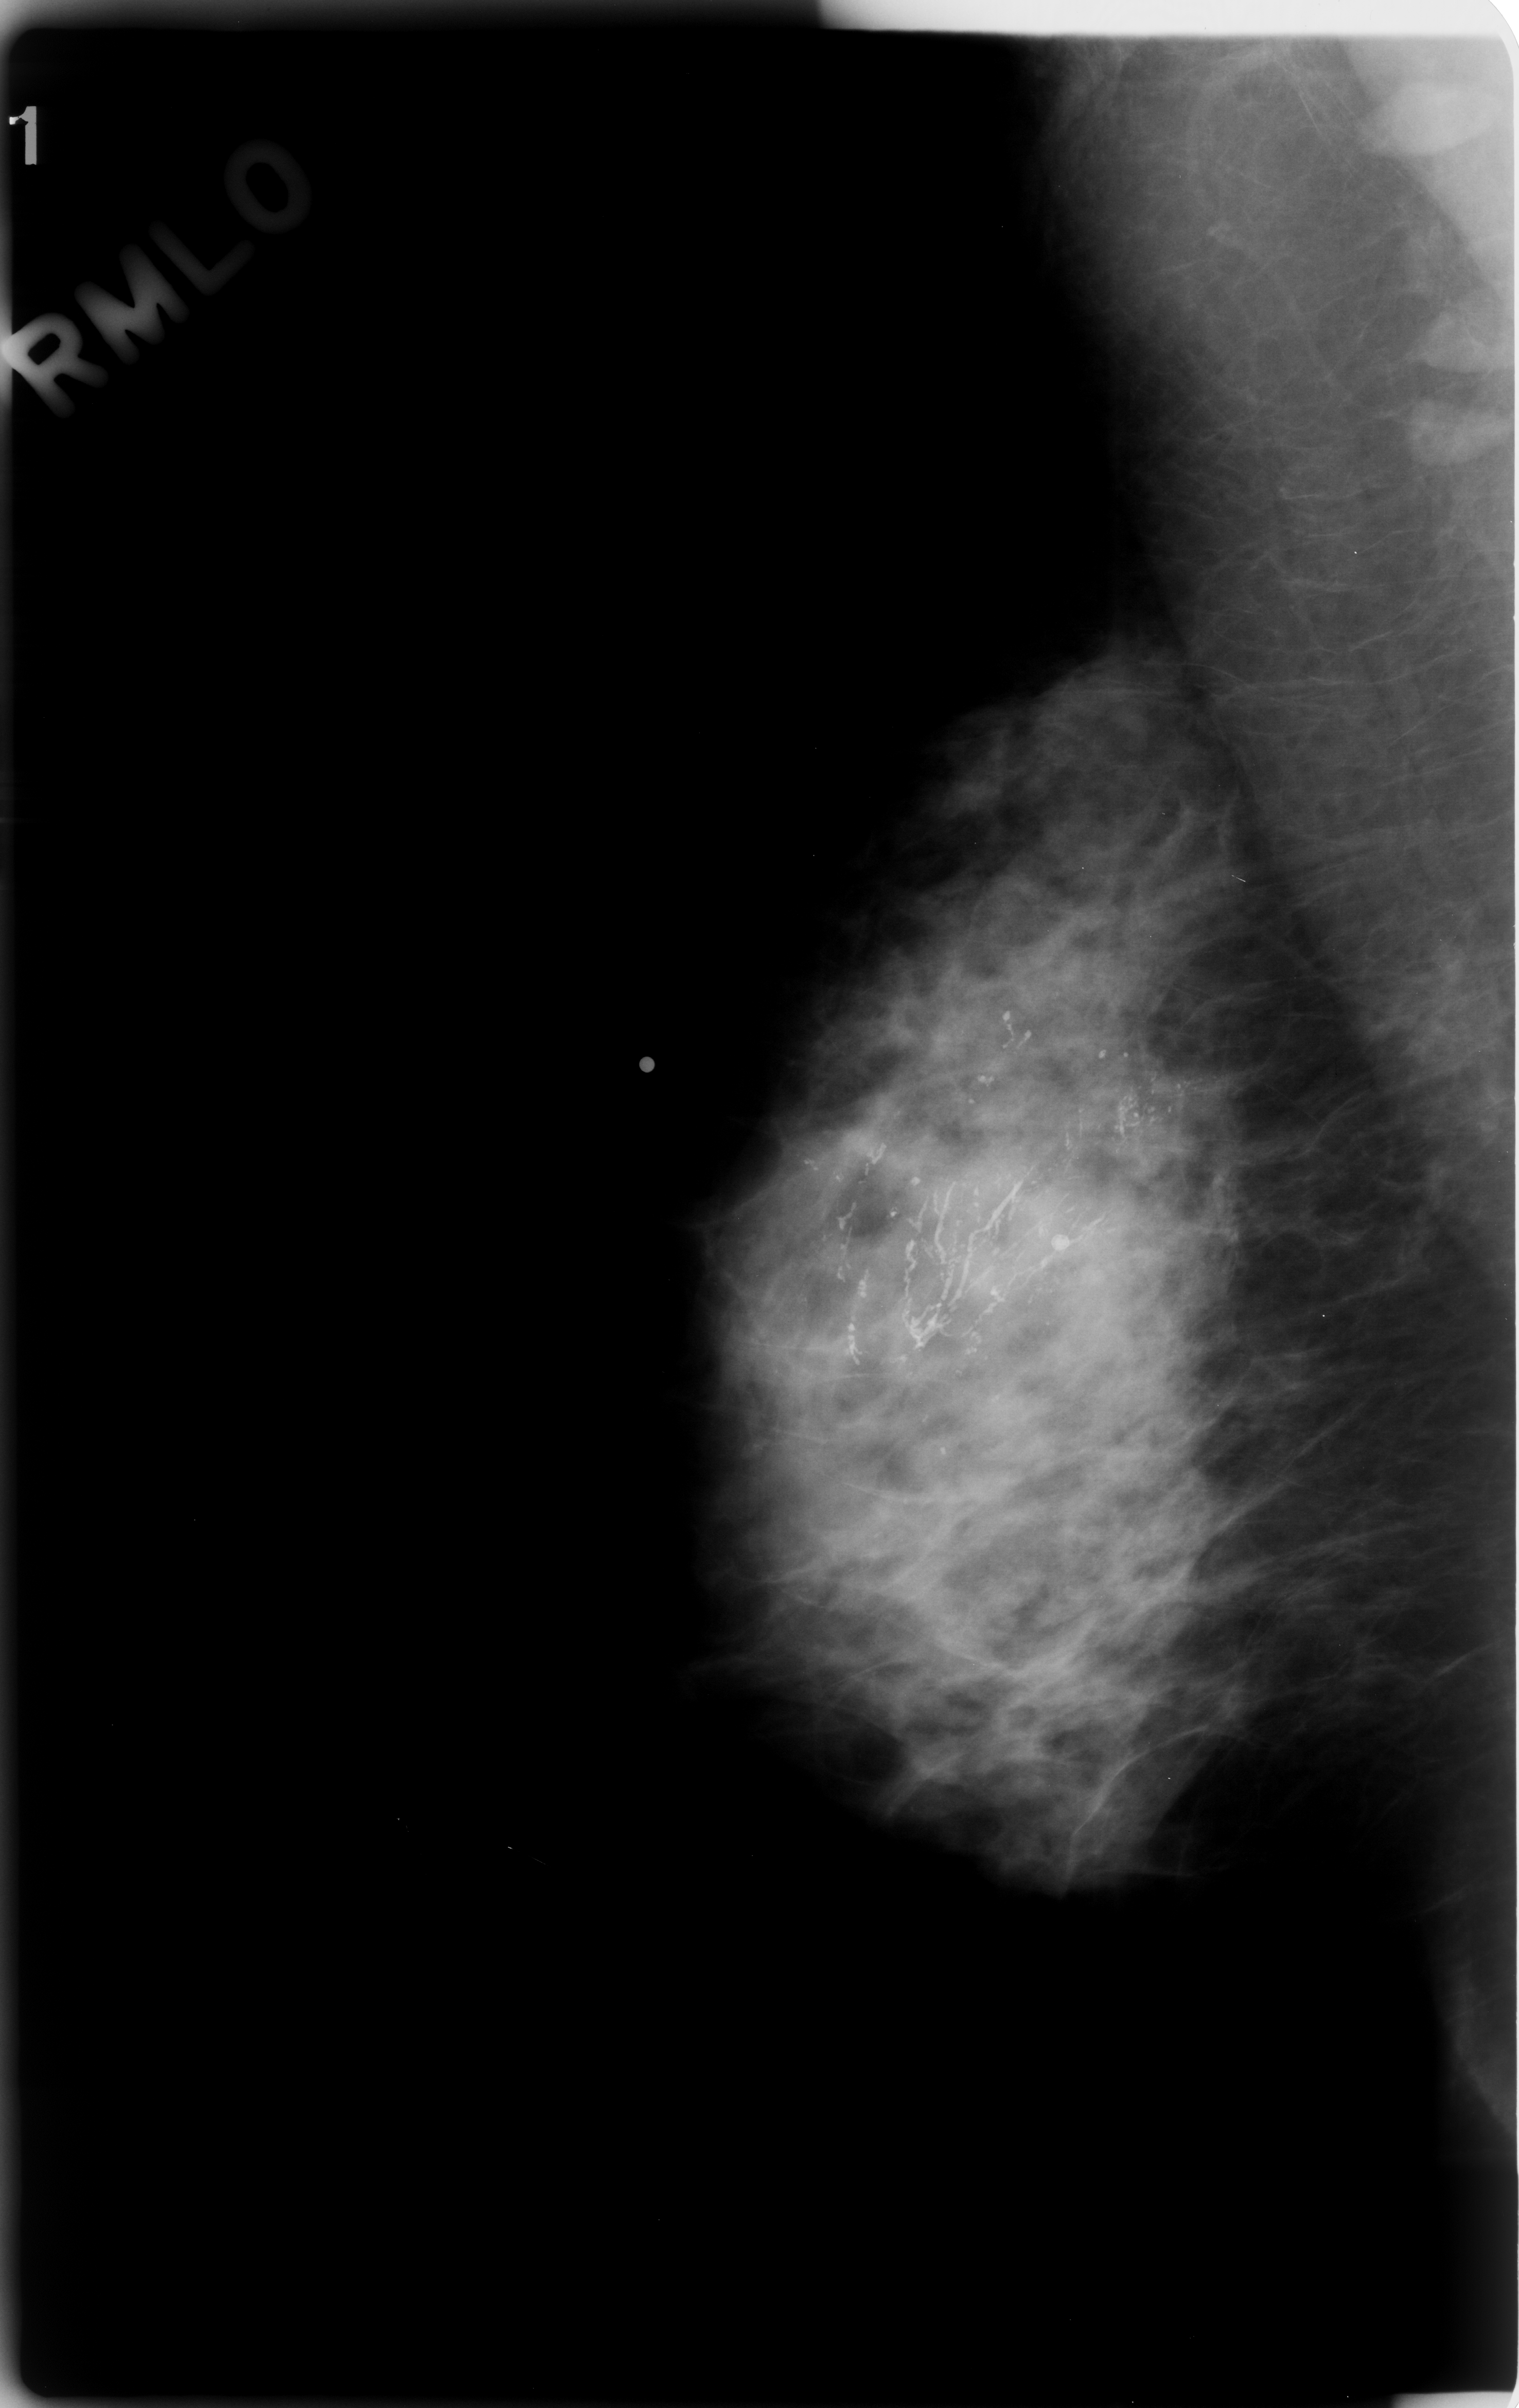
Scanned film-screen mammogram; right breast; mediolateral oblique (MLO) view; BI-RADS breast density category 3 (scale 1–4).
Marked abnormality: calcifications, morphology fine linear branching, distribution segmental; BI-RADS assessment category 5; subtlety rating 5 on a 1 (subtle) to 5 (obvious) scale; pathology (as recorded): malignant.